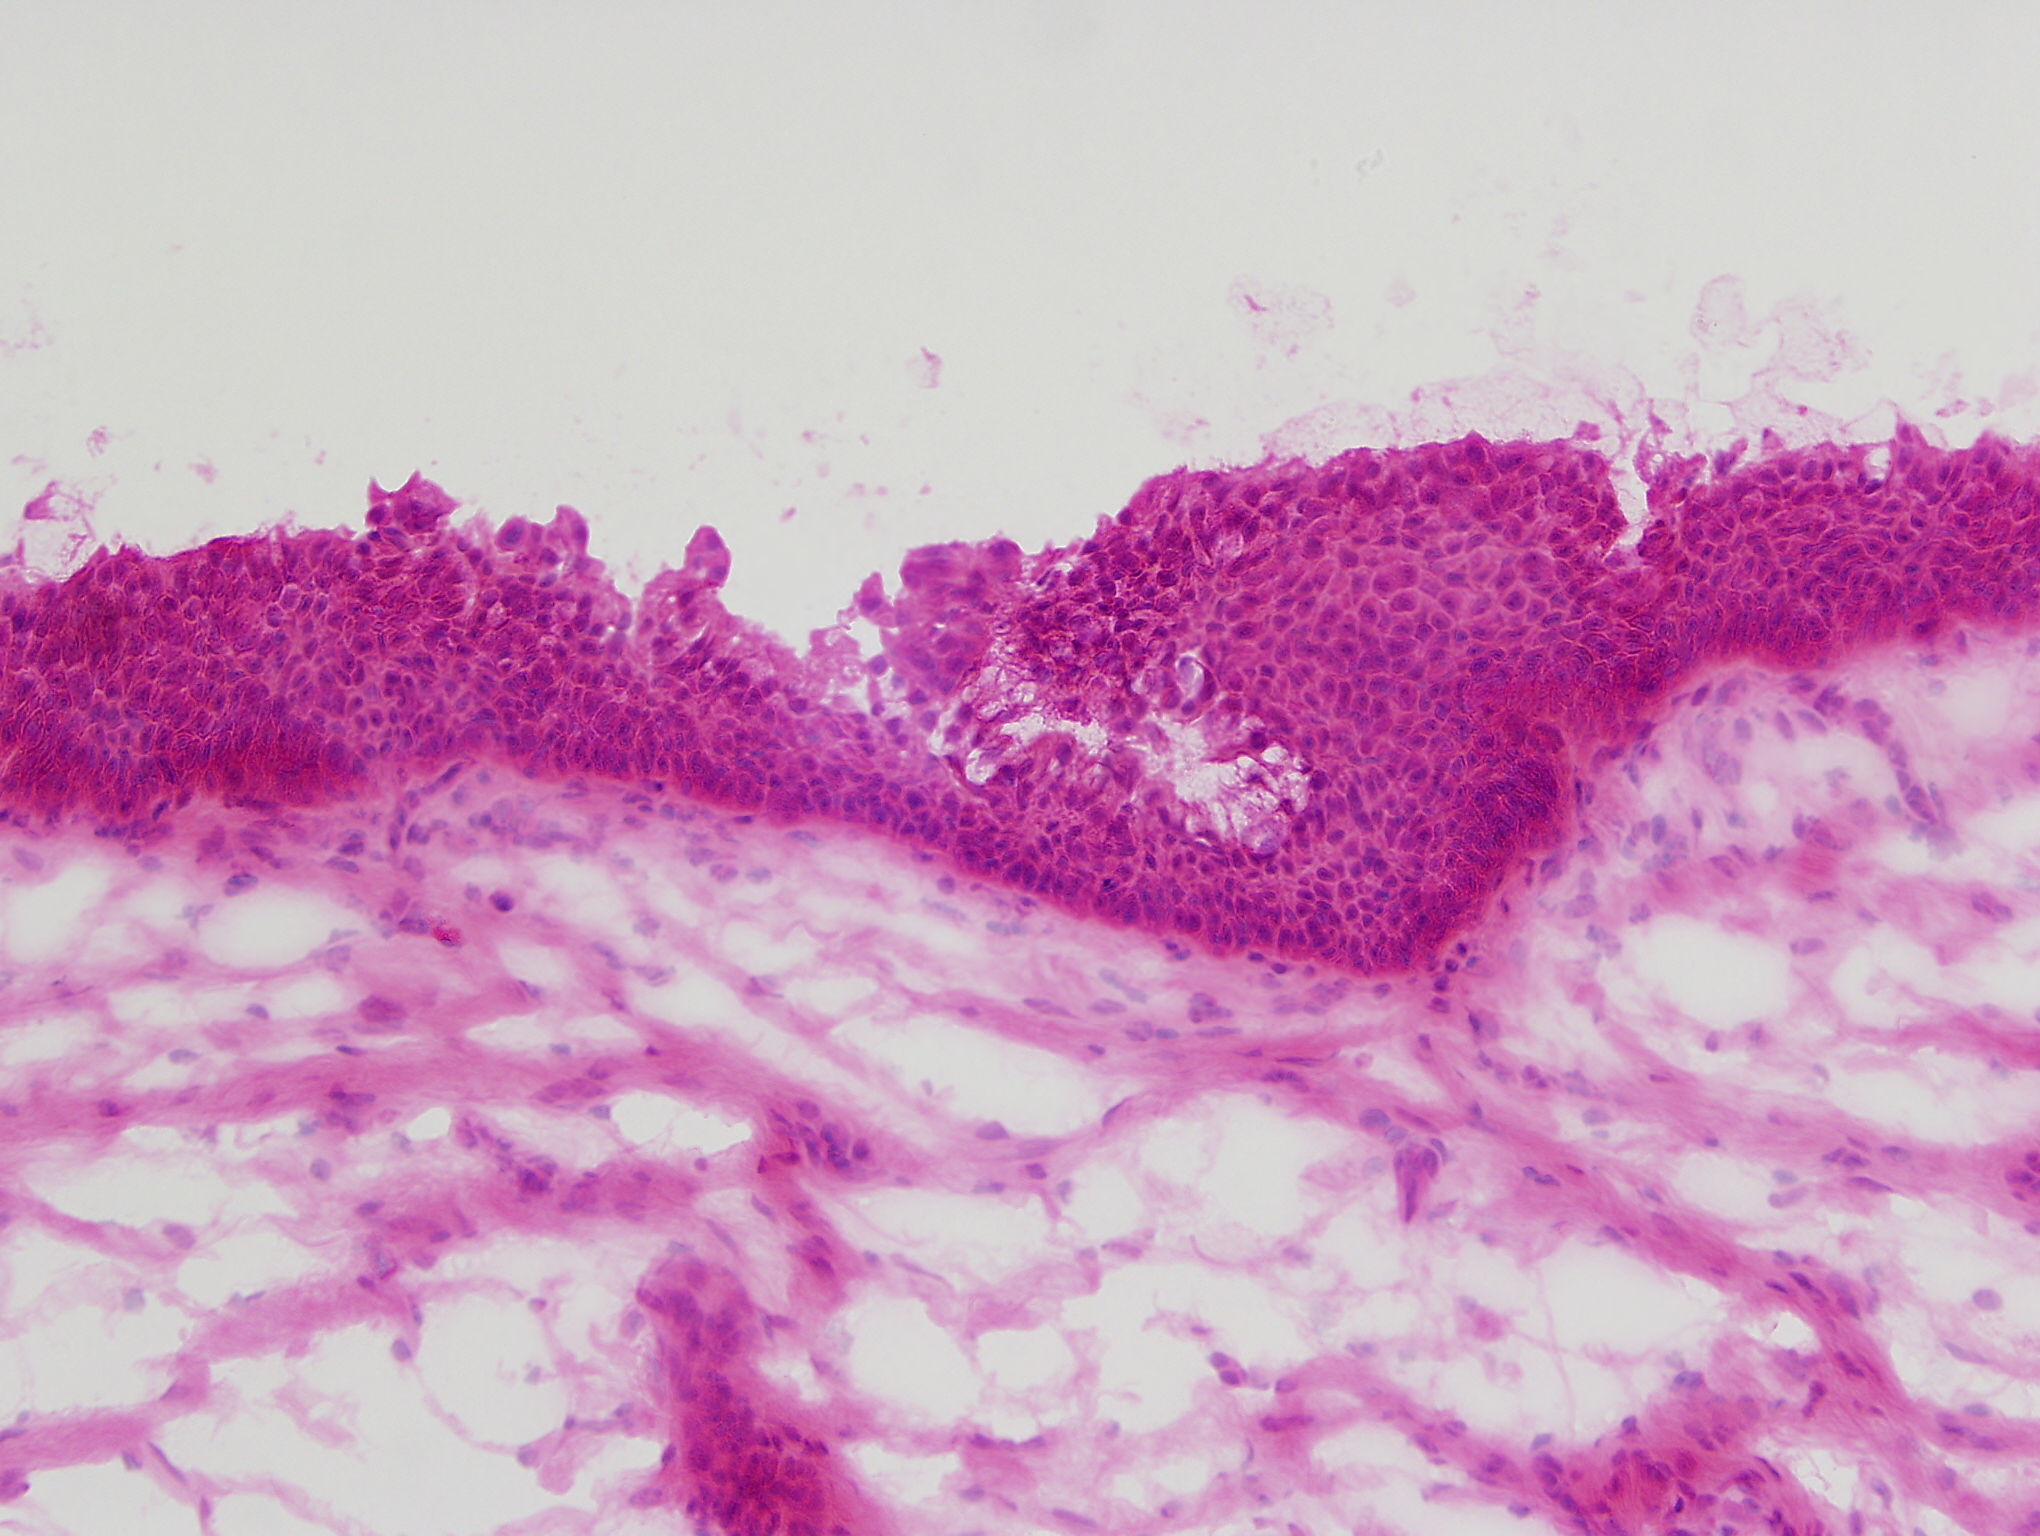
Single-field H&E-stained photomicrograph, roughly 1.0 x 0.8 mm in extent. Frozen section from the top of the tissue portion. Solid tissue normal (non-tumour tissue) sample from the head and neck. Patient: male, age at initial diagnosis 38 years.
• this section: solid tissue normal (non-tumour) sample from the same patient
• patient diagnosis: Squamous cell carcinoma, NOS